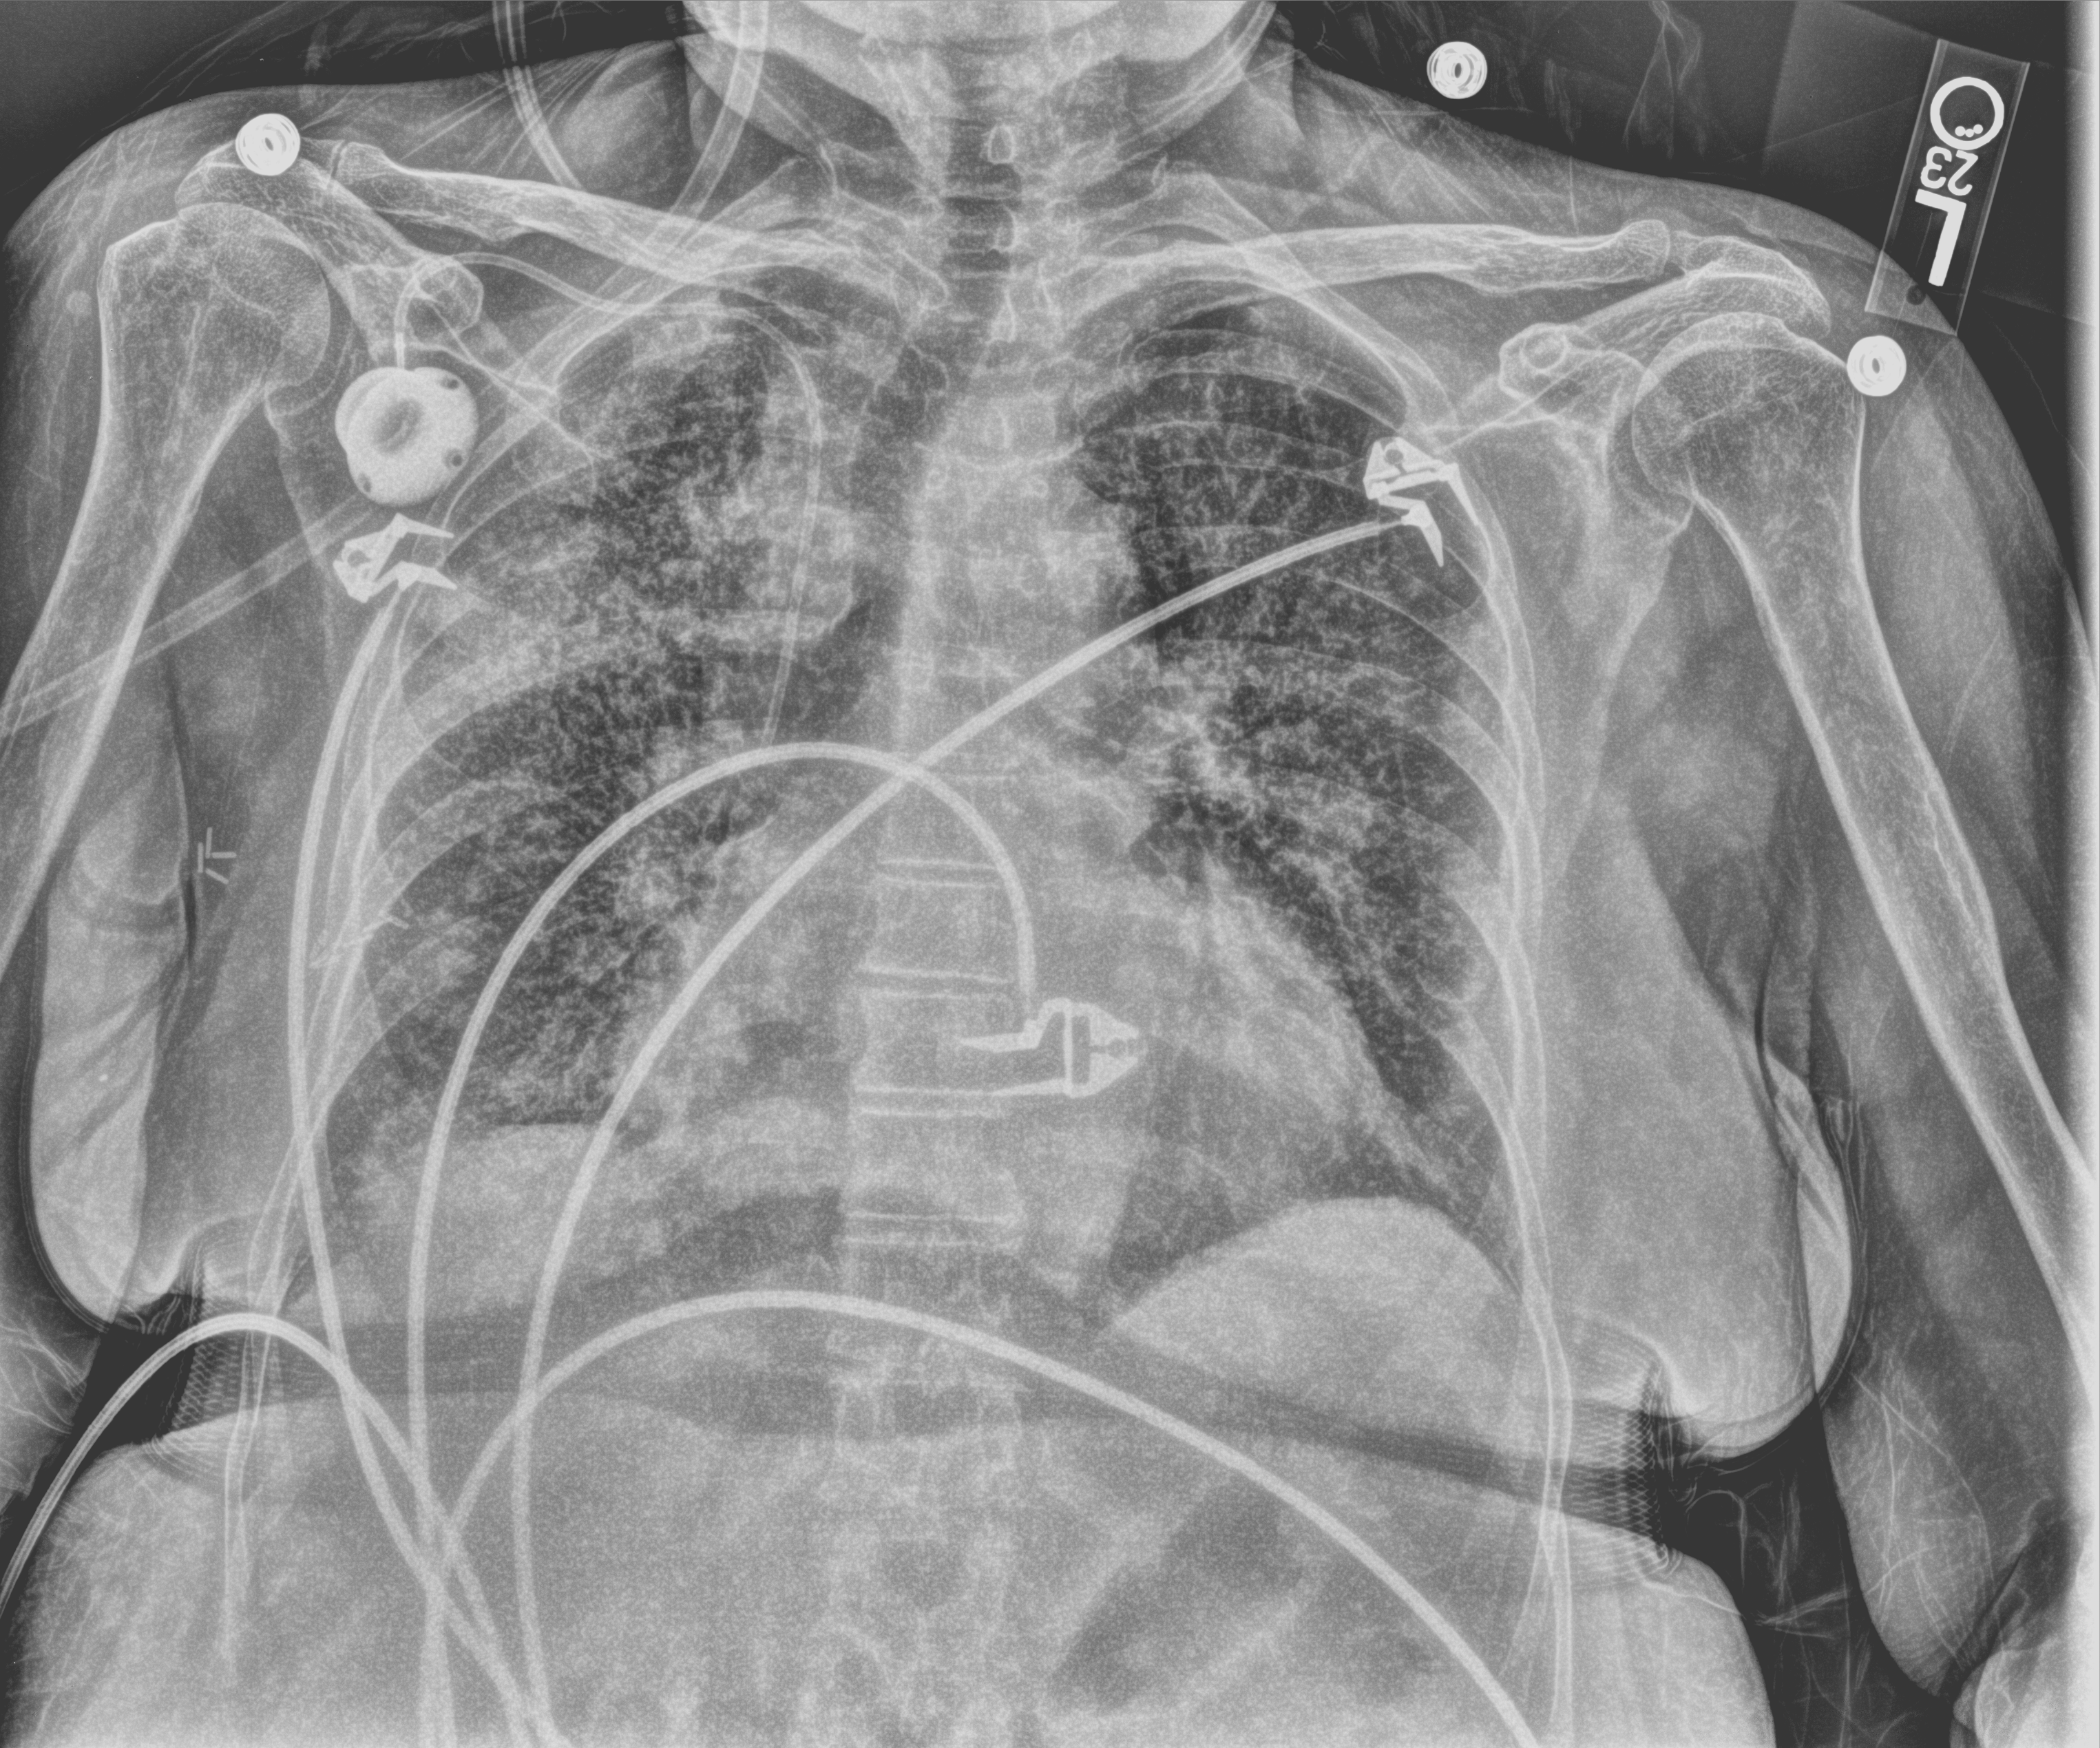
Bedside chest radiograph (computed radiography); anteroposterior (AP) projection. Female patient hospitalised with COVID-19, age 60–74 years.
From the hospital-stay record, not from the radiograph (when in the stay this image was taken is not recorded):
- mechanically ventilated during this hospital stay: yes
- admitted to intensive care during this hospital stay: yes